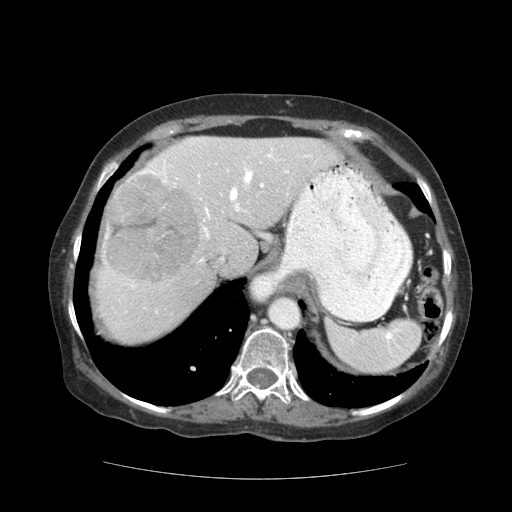
Contrast-enhanced abdominal CT (liver protocol), one axial slice. Slice 88 of 111 in the series (ordered by position). Reconstruction kernel STANDARD. 140 kVp. Soft-tissue window (W 400 / L 40 HU). 2.5 mm slice thickness. 512 × 512 image matrix, field of view 360 × 360 mm. Case-level facts recorded for this patient, not image findings: diagnosis: hepatocellular carcinoma (patient treated with transarterial chemoembolisation; whether this scan precedes or follows treatment is not stated here); TNM stage (as recorded): Stage-I; Child-Pugh class: A; tumour differentiation: moderately-poorly differentiated.
Structures marked on this image (semi-automatic segmentation, software-assisted and operator-edited):
- liver parenchyma outside the tumour (the mass and vessels are separate outlines, so this box may not span the whole liver): bounding box [x1, y1, x2, y2] px = [96, 136, 338, 344]
- mass: [105, 173, 201, 286]
- liver vessels: [105, 139, 310, 313]